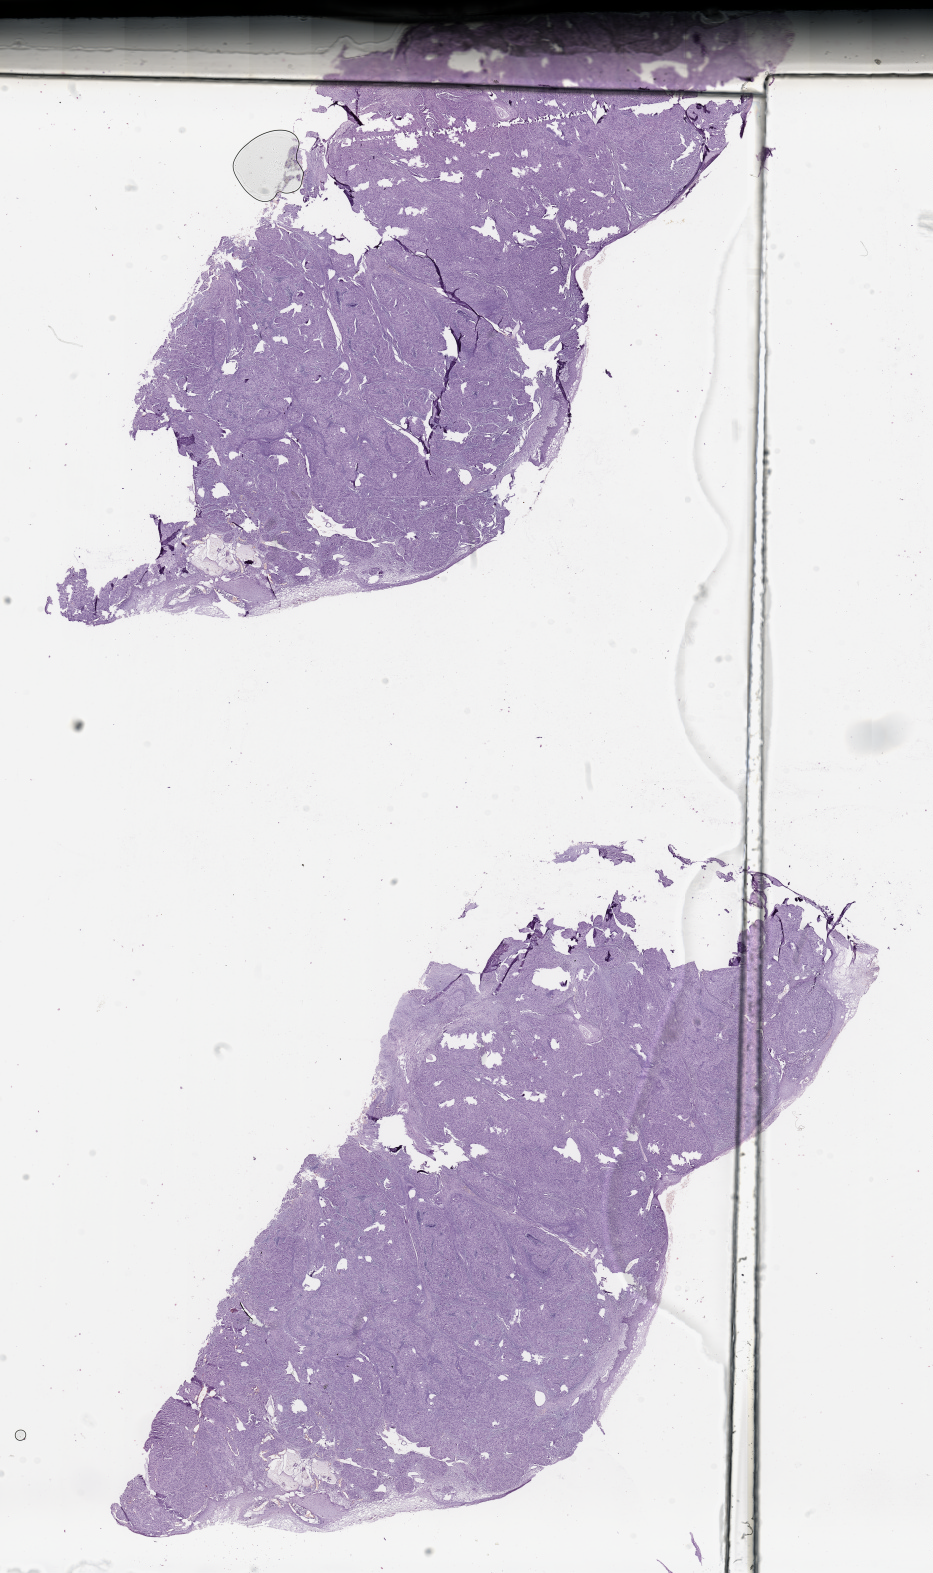
H&E whole-slide image, a low-resolution overview of the entire scanned area, about 14.8 x 24.9 mm (acquisition: 20x scan), tumour tissue sample, sampled site: tongue. 64-year-old male patient. Histologic grade: G2 (moderately differentiated). Slide review estimates, as recorded: tumour nuclei 90%, necrosis 0%.
- primary tumour site (as recorded): oropharynx
- AJCC pathologic stage: III
- diagnosis: Squamous cell carcinoma, NOS (base of tongue, NOS)